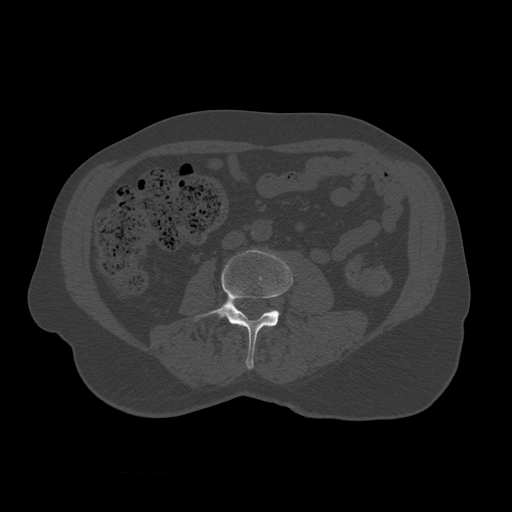
CT including the spine, one axial slice. Slice 300 of 450 in the series (ordered by position). Reconstruction kernel STANDARD. 120 kVp. Bone window (W 1800 / L 400 HU). 1.25 mm slice thickness. 512 × 512 image matrix, field of view 405 × 405 mm. Patient age 75 years. Case-level facts recorded for this patient, not image findings: primary cancer: prostate.
Structures marked on this image (semi-automatic segmentation, software-assisted and operator-edited):
- L3 vertebra: bounding box [x1, y1, x2, y2] px = [195, 249, 294, 370]